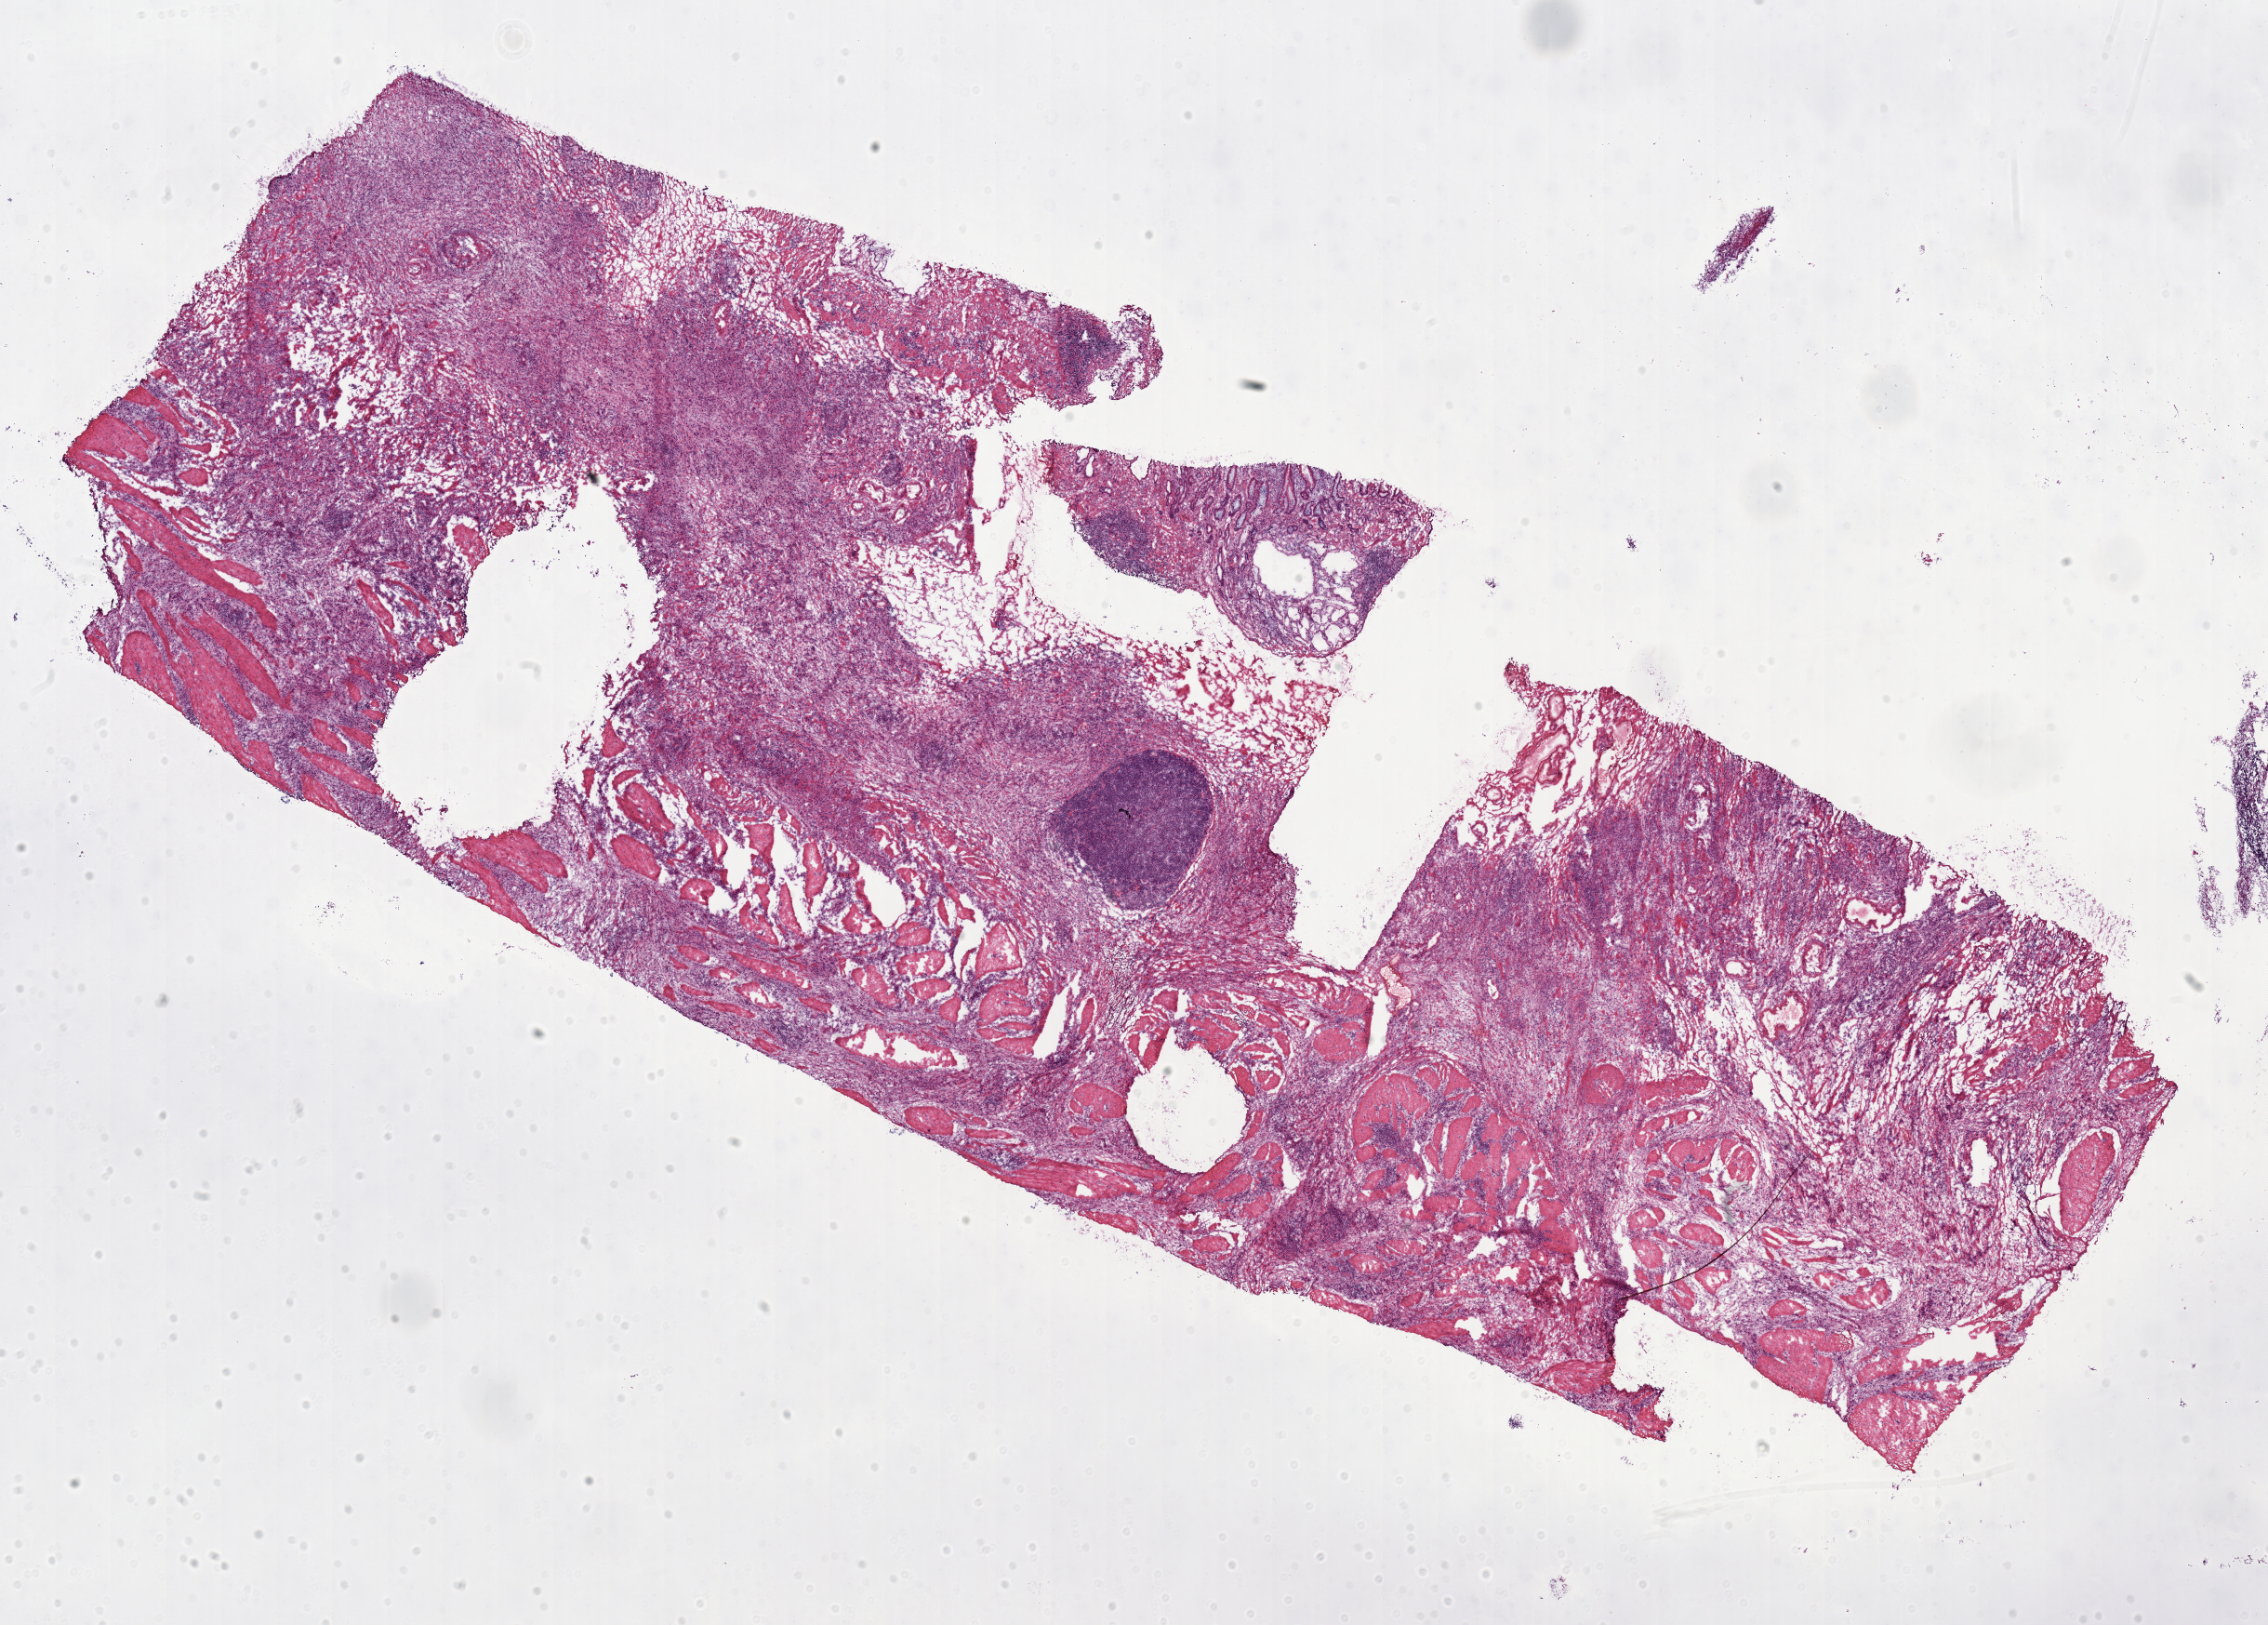
H&E-stained whole-slide image — shown as a low-resolution overview of the whole scanned area (about 19.4 x 13.9 mm, slide scanned at 20x). Frozen section from the top of the tissue portion. Sample: primary tumour, stomach. Female patient; age at initial diagnosis 78 years. Histologic grade: G3 (poorly differentiated). Pathologist review of this section (percent, as recorded): tumour cells 50%, tumour nuclei 60%, normal cells 40%, stromal cells 10%, necrosis 0%.
- histologic diagnosis: Adenocarcinoma, NOS (gastric antrum)
- AJCC pathologic stage: II
- TNM: T3 N0 M0